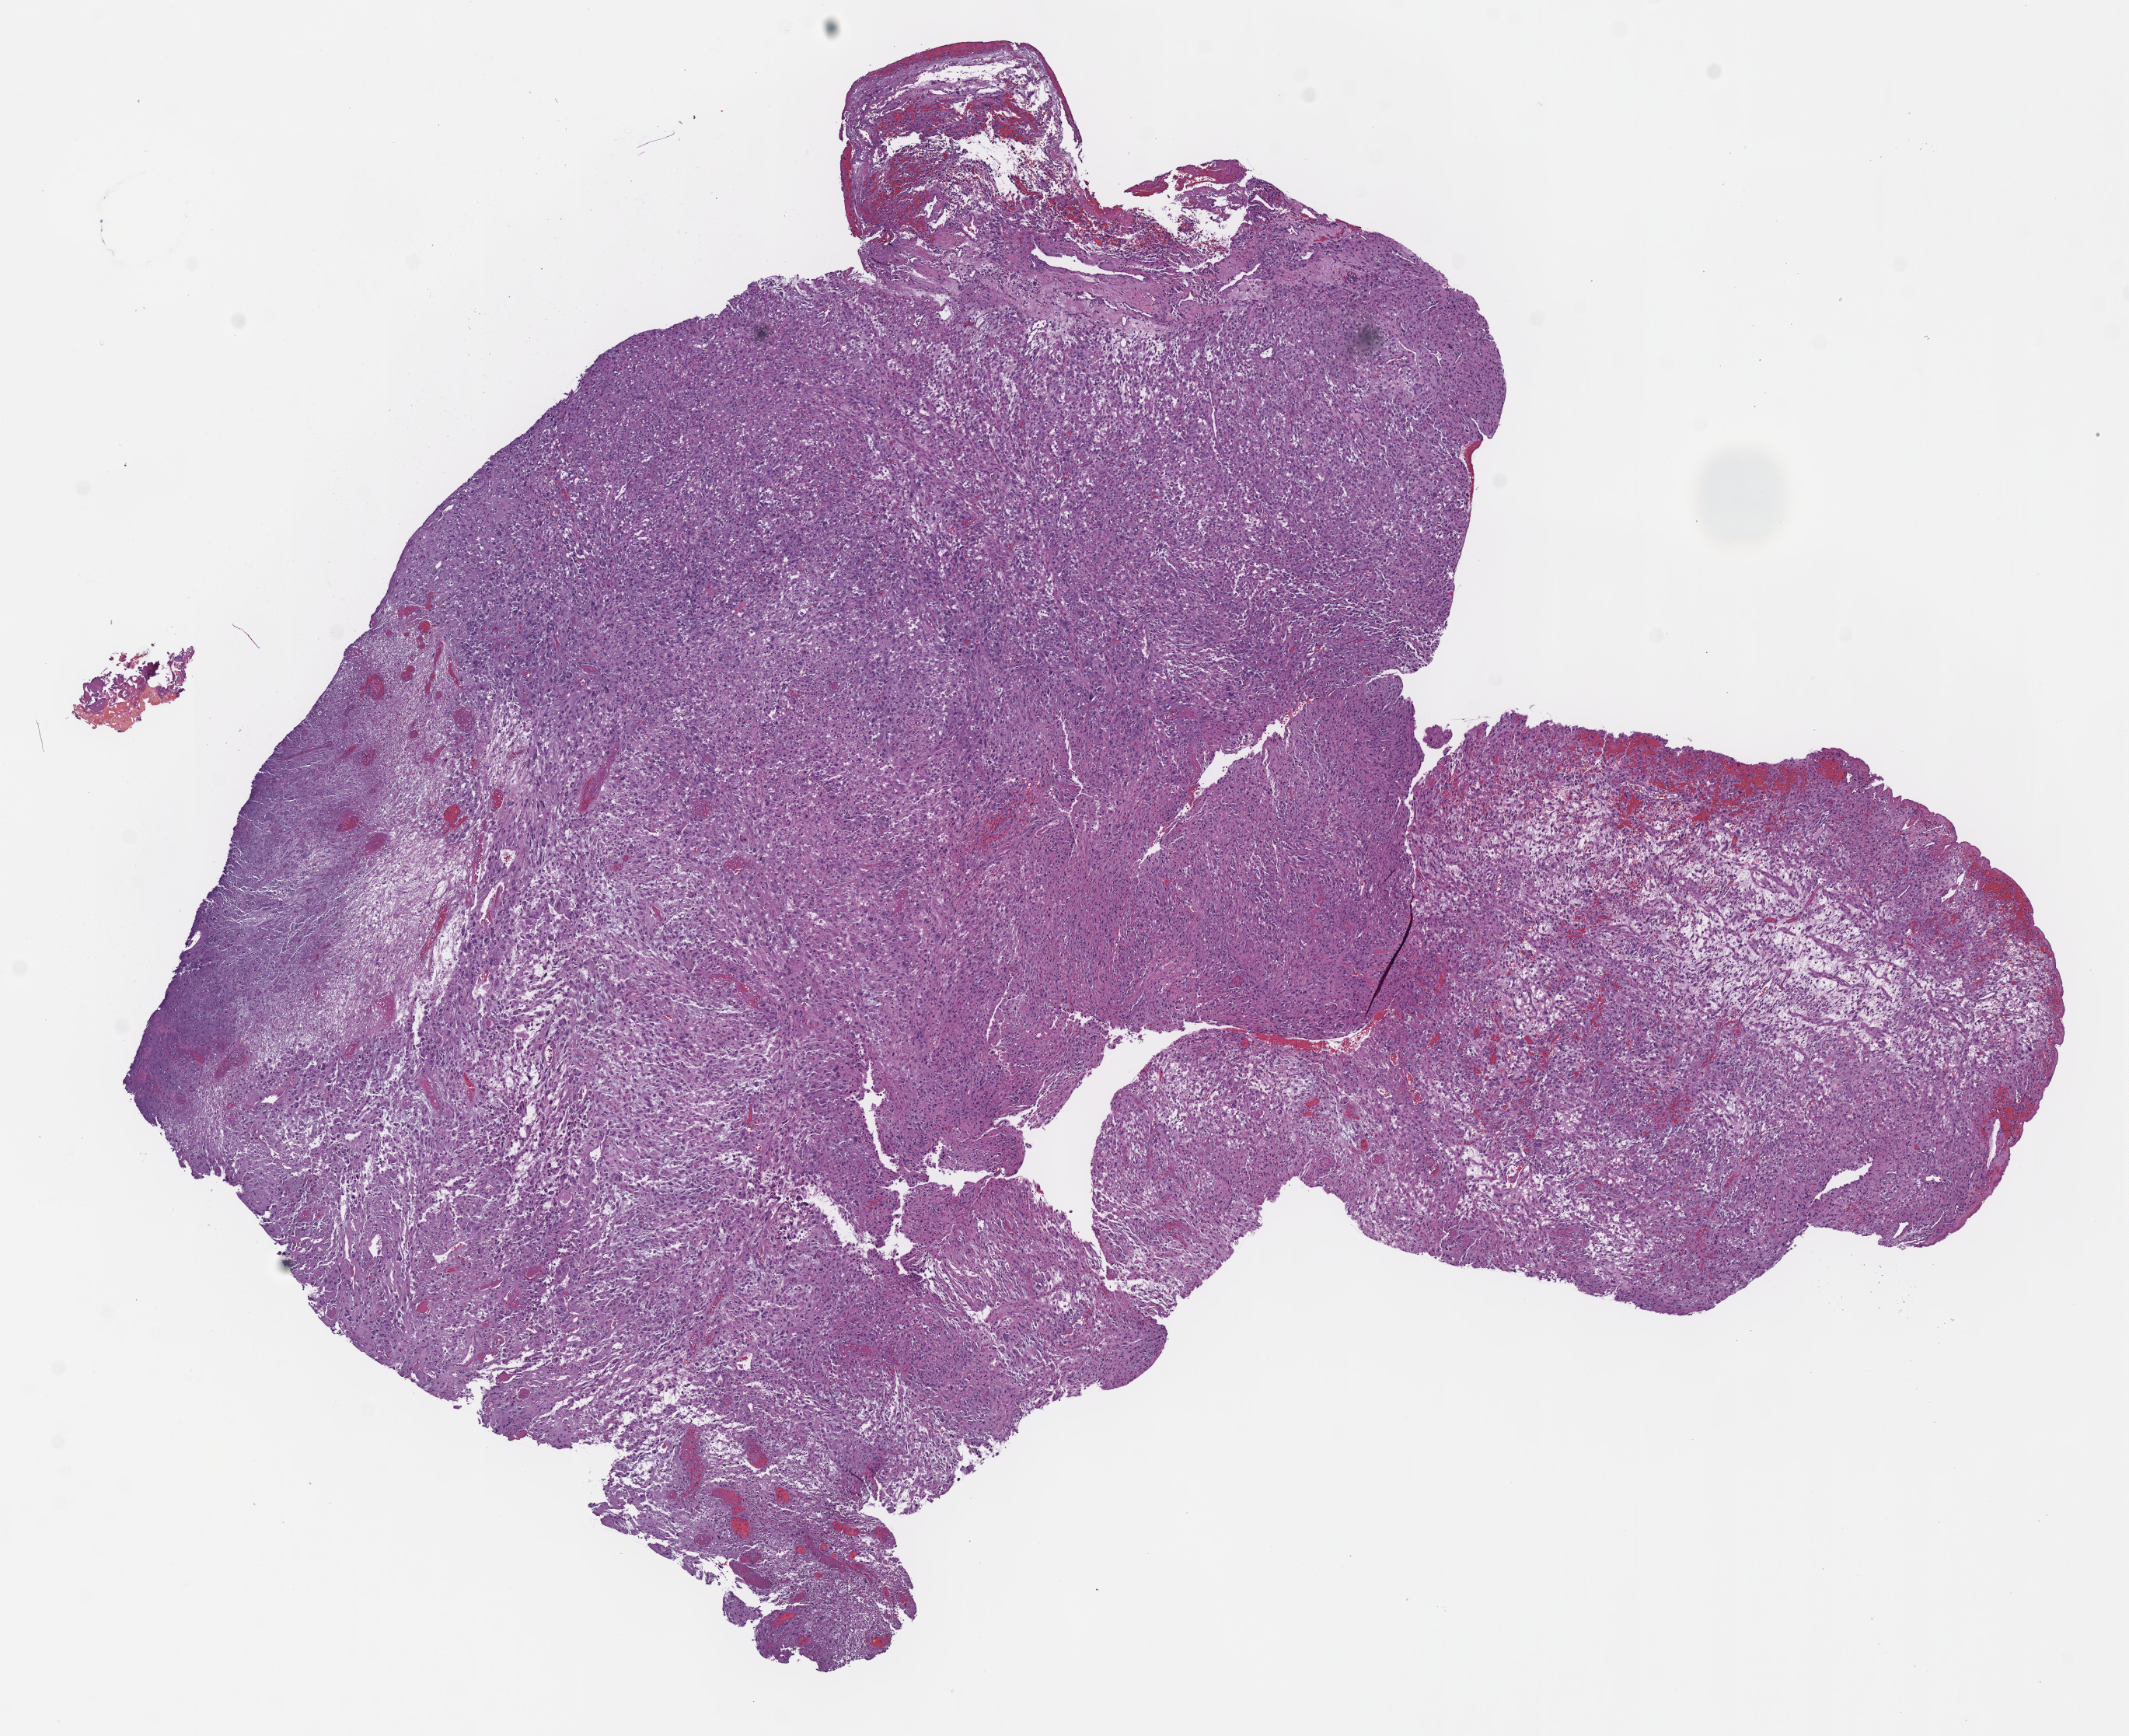
Whole-slide histology image, H&E-stained, a low-resolution overview of the entire scanned area, about 10.8 x 8.8 mm; FFPE section; sample: primary tumour, ovary. Patient: female, age at initial diagnosis 65 years.
Diagnosis: Leiomyosarcoma, NOS.